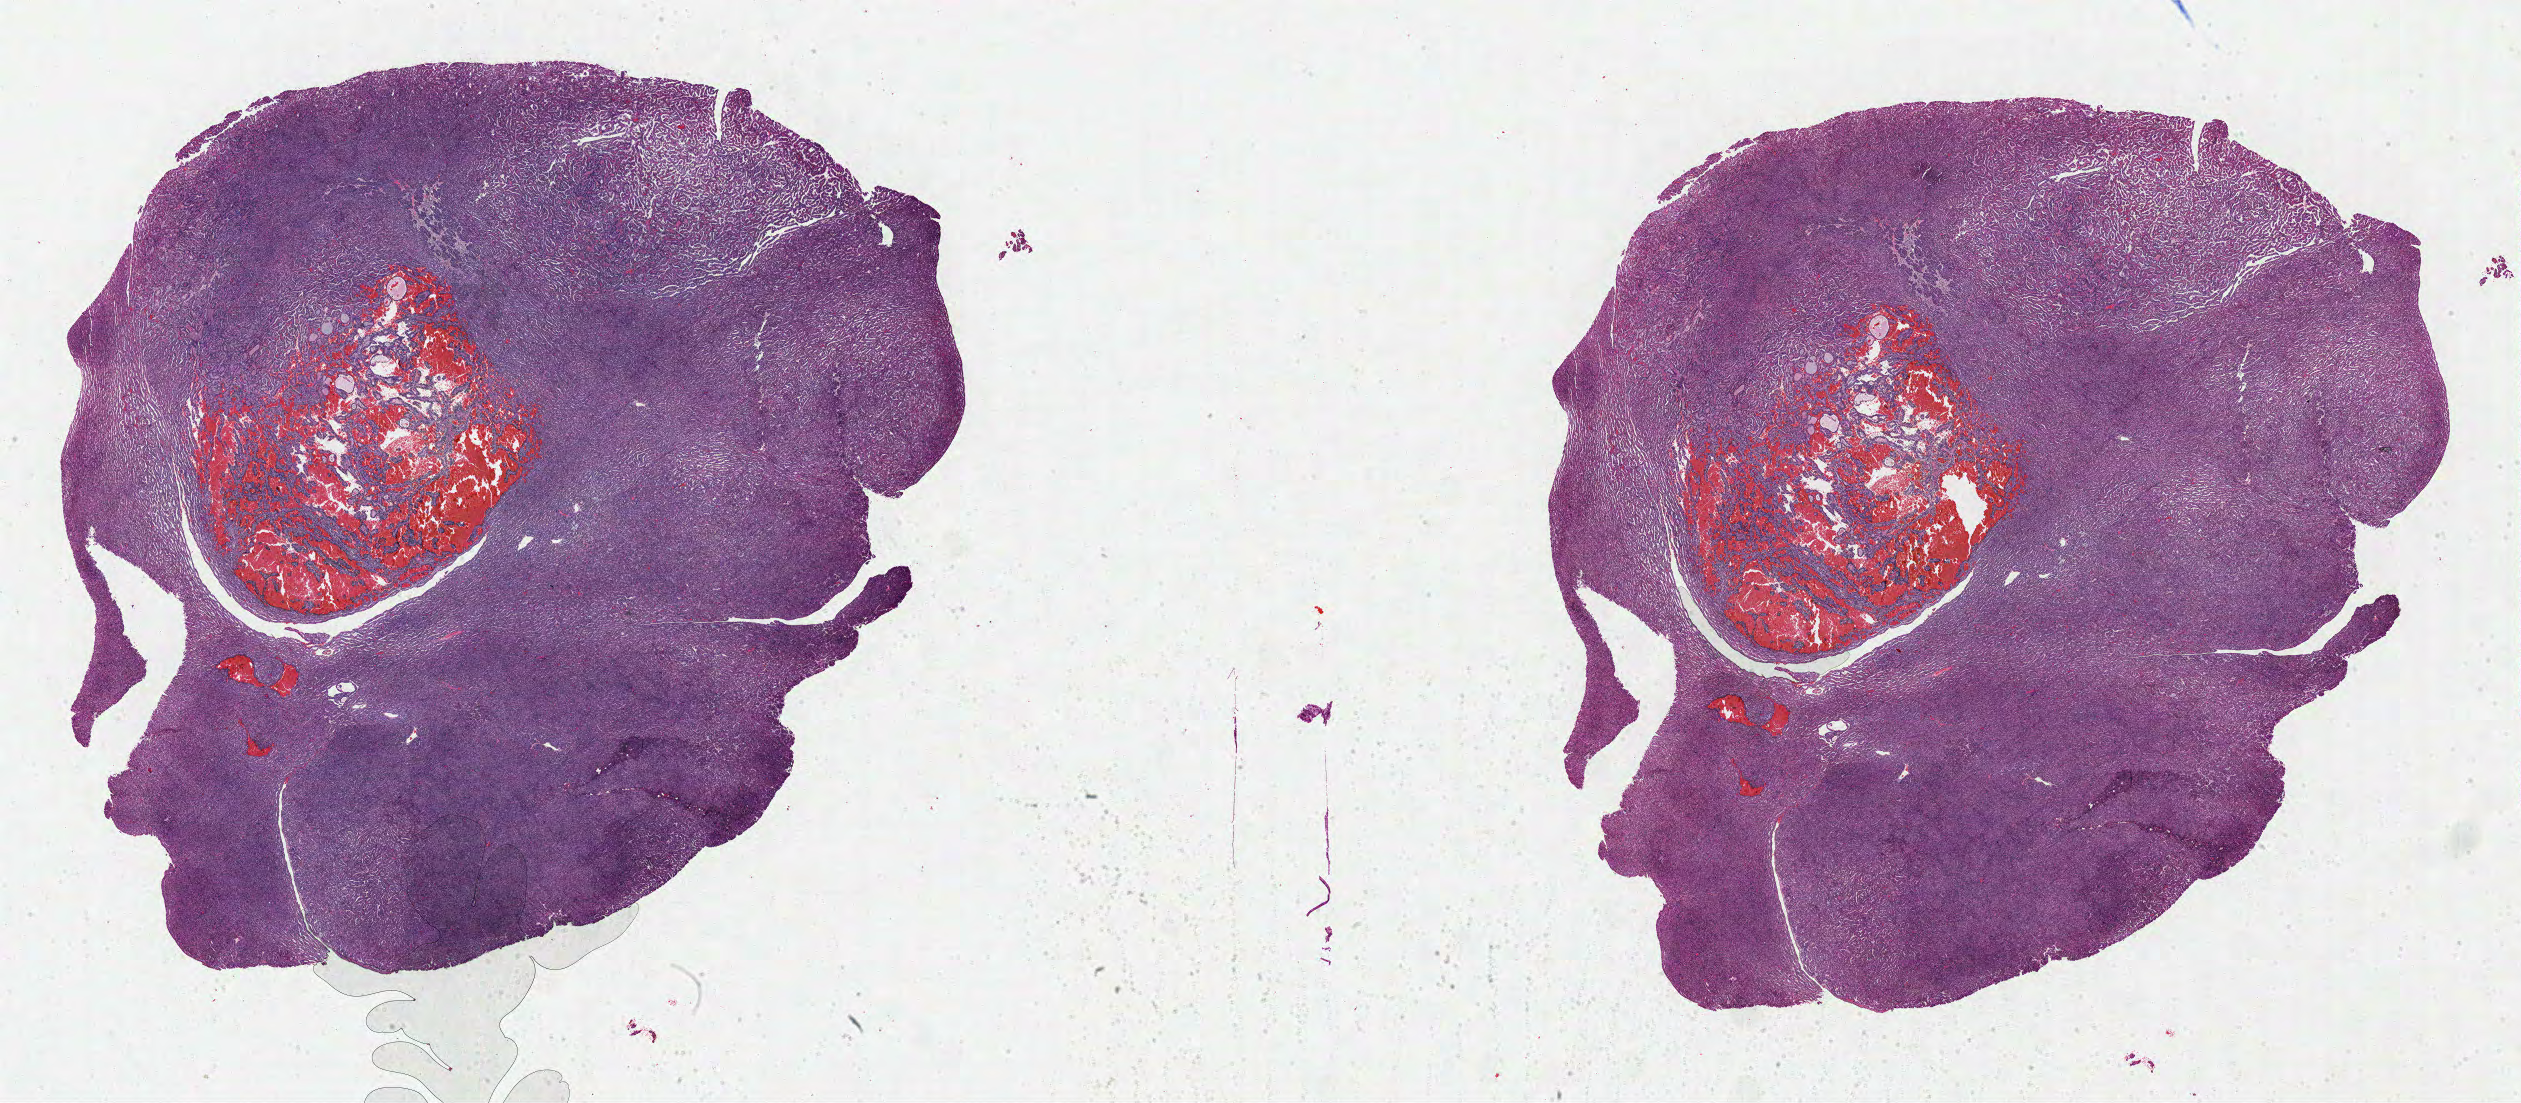
Digitized H&E-stained tissue section (whole slide), whole scanned area (about 39.6 x 17.3 mm, acquisition: 40x scan) shown as a low-resolution overview. Formalin-fixed paraffin-embedded (FFPE) diagnostic section. Sample: primary tumour, kidney. Patient: male, age at initial diagnosis 71 years.
• AJCC pathologic stage: III
• TNM: T3a NX
• histologic diagnosis: Papillary adenocarcinoma, NOS